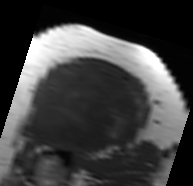
MRI of an extremity soft-tissue mass, one axial slice; slice 52 of 91 in the series (ordered by position); MR volume resampled by the dataset authors to the PET/CT grid (not the native acquisition matrix); 3.27 mm slice thickness; 193 × 186 image matrix. Female patient. From the clinical record (not read from this slice): histological type: malignant solitary fibrous tumor; grade: intermediate; site of the primary tumour: right thigh.
Structures marked on this image (expert contour drawn on MRI and transferred to this co-registered scan by the dataset authors):
- gross tumour volume including surrounding oedema: bounding box <22,62,146,152> (left, top, right, bottom; pixels)
- gross tumour volume (mass): <22,64,141,150>